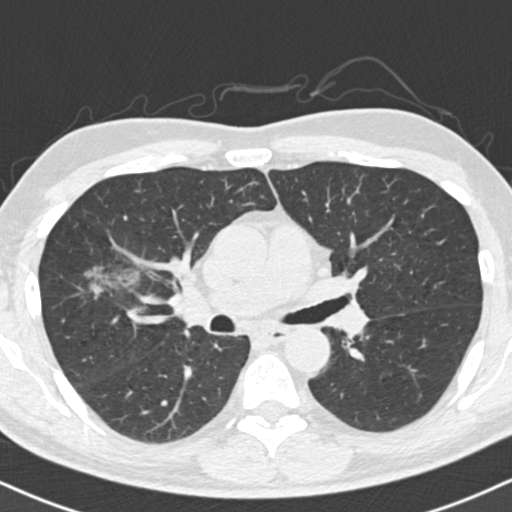
Low-dose screening chest CT, axial slice, first (baseline) screen, lung window (W 1500 / L -600 HU), 2 mm slice thickness, 120 kVp, slice 65 of 154 in the series. Male participant, aged 56 years at enrolment. Former smoker at enrolment.
Expert-annotated lung lesion, bounding box (x1, y1, x2, y2) in pixels: (60, 252, 151, 318). No non-calcified nodule or mass ≥4 mm was recorded by the screening reader at this exam. Official screen result: negative screen, minor abnormalities not suspicious for lung cancer. Lung cancer was diagnosed 392 days after this screen: bronchiolo-alveolar adenocarcinoma, NOS, right upper lobe, well differentiated (G1), stage IIB (AJCC 6th edition), 30 mm at pathology.